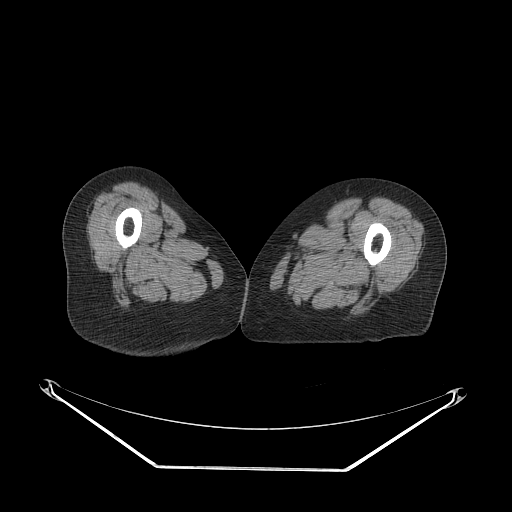
CT of an extremity soft-tissue mass (from a PET/CT study), one axial slice; 140 kVp; soft-tissue window (W 400 / L 40 HU); 3.75 mm slice thickness; 512 × 512 image matrix, field of view 500 × 500 mm. Female patient. From the clinical record (not read from this slice): histological type: pleomorphic leiomyosarcoma; grade: high; site of the primary tumour: left thigh.
Outlined on this slice (expert contour drawn on MRI and transferred to this co-registered scan by the dataset authors):
- gross tumour volume including surrounding oedema: box from (x=283, y=212) to (x=298, y=220) px